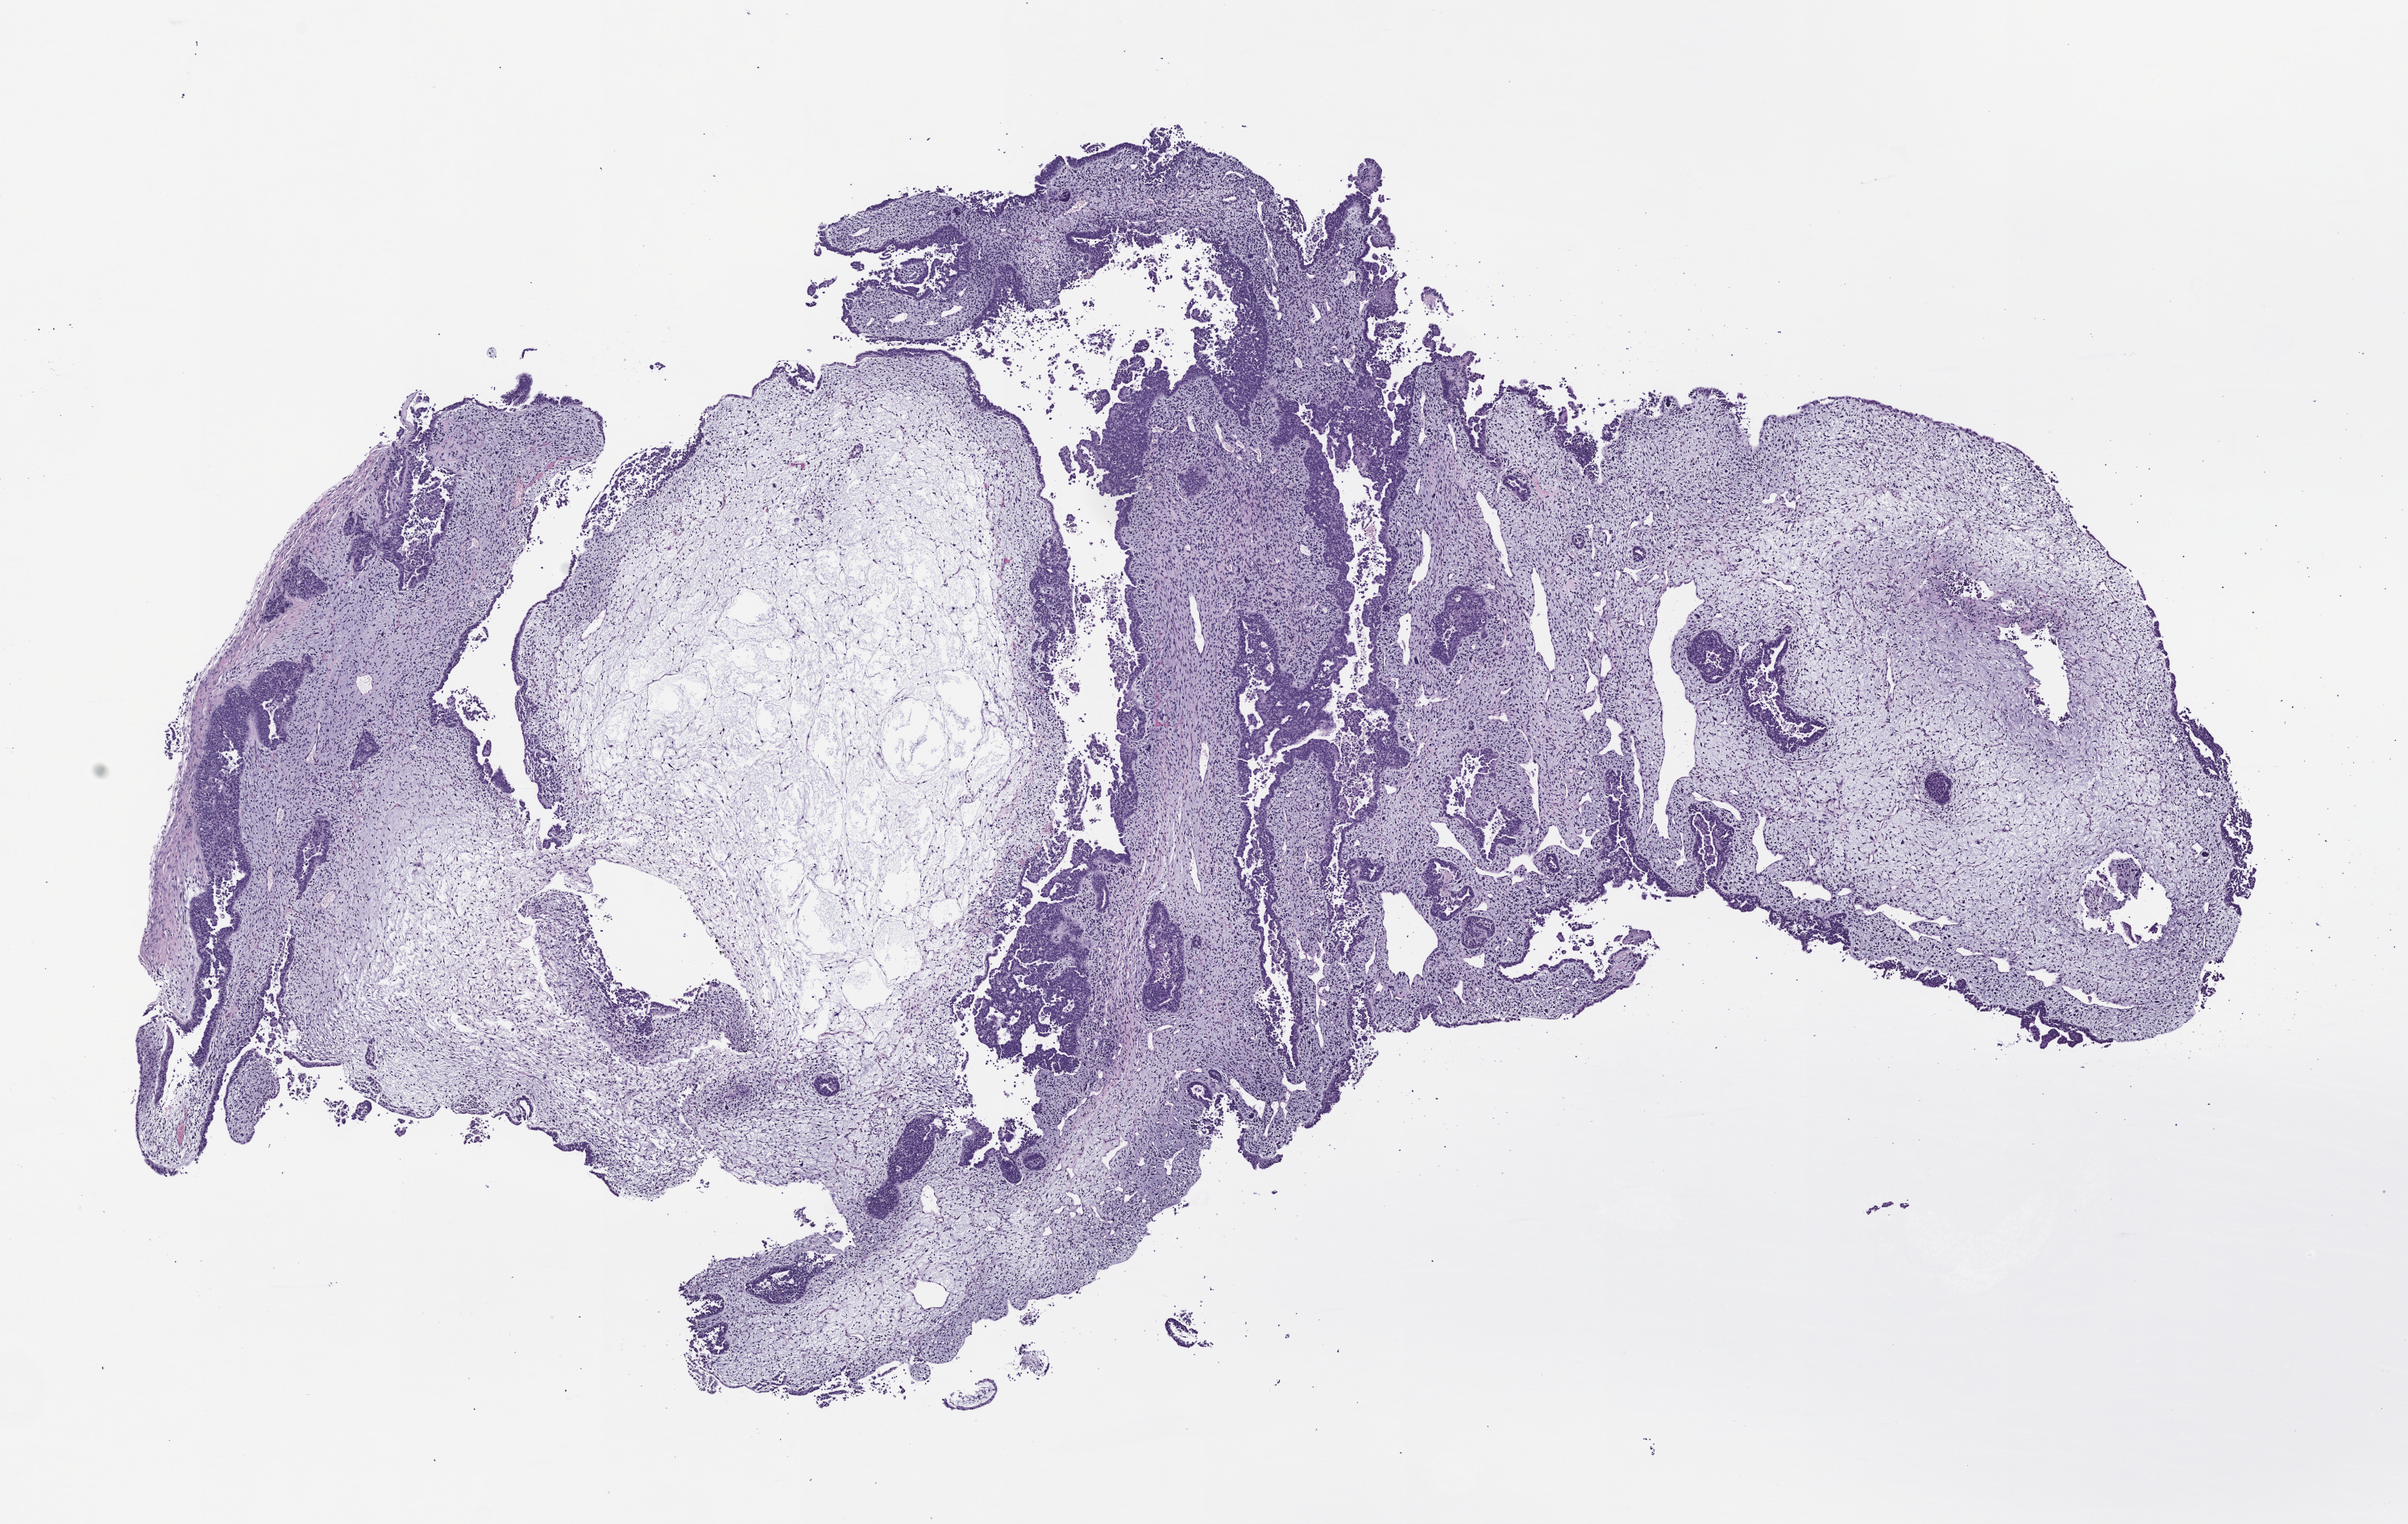
H&E whole-slide image of a patient-derived xenograft (PDX) tumor grown in a mouse, a low-resolution overview of the entire scanned area, about 12.0 x 7.6 mm, FFPE section, tumor site category: uterus.
Originating patient diagnosis: Carcinosarcoma.